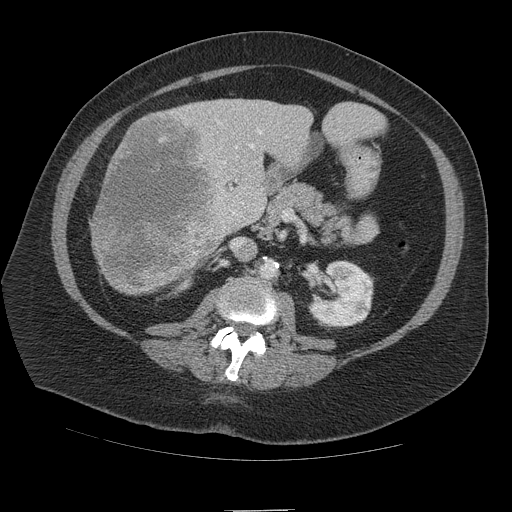
Contrast-enhanced abdominal CT (liver protocol), one axial slice; slice 44 of 109 in the series (ordered by position); 140 kVp; soft-tissue window (W 400 / L 40 HU); 2.5 mm slice thickness; 512 × 512 image matrix. Case-level facts recorded for this patient, not image findings: diagnosis: hepatocellular carcinoma (patient treated with transarterial chemoembolisation; whether this scan precedes or follows treatment is not stated here); TNM stage (as recorded): Stage-IVB; Child-Pugh class: A; tumour differentiation: poorly differentiated; tumour nodularity: multinodular.
Structures marked on this image (semi-automatic segmentation, software-assisted and operator-edited):
- liver parenchyma outside the tumour (the mass and vessels are separate outlines, so this box may not span the whole liver): bounding box <91,98,374,294> (left, top, right, bottom; pixels)
- mass: <90,112,227,294>
- liver vessels: <216,120,262,215>